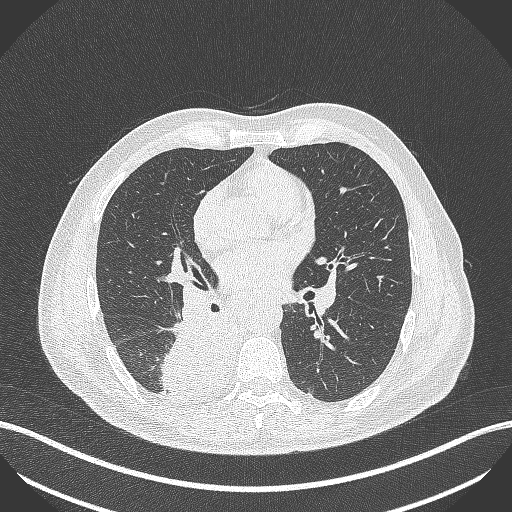
Chest CT, one axial slice. Slice 243 of 451 in the series (ordered by position). 100 kVp. Lung window (W 1500 / L -600 HU). 1 mm slice thickness. 512 × 512 image matrix, field of view 400 × 400 mm. Male patient, age 61 years. From the clinical record (not read from this slice): clinical TNM (as recorded): T1 N0 M0.
Annotated regions visible in this slice (rectangle marked by the reading radiologist):
- lung tumour (recorded histology: small cell carcinoma): bounding box <162,315,240,400> (left, top, right, bottom; pixels)